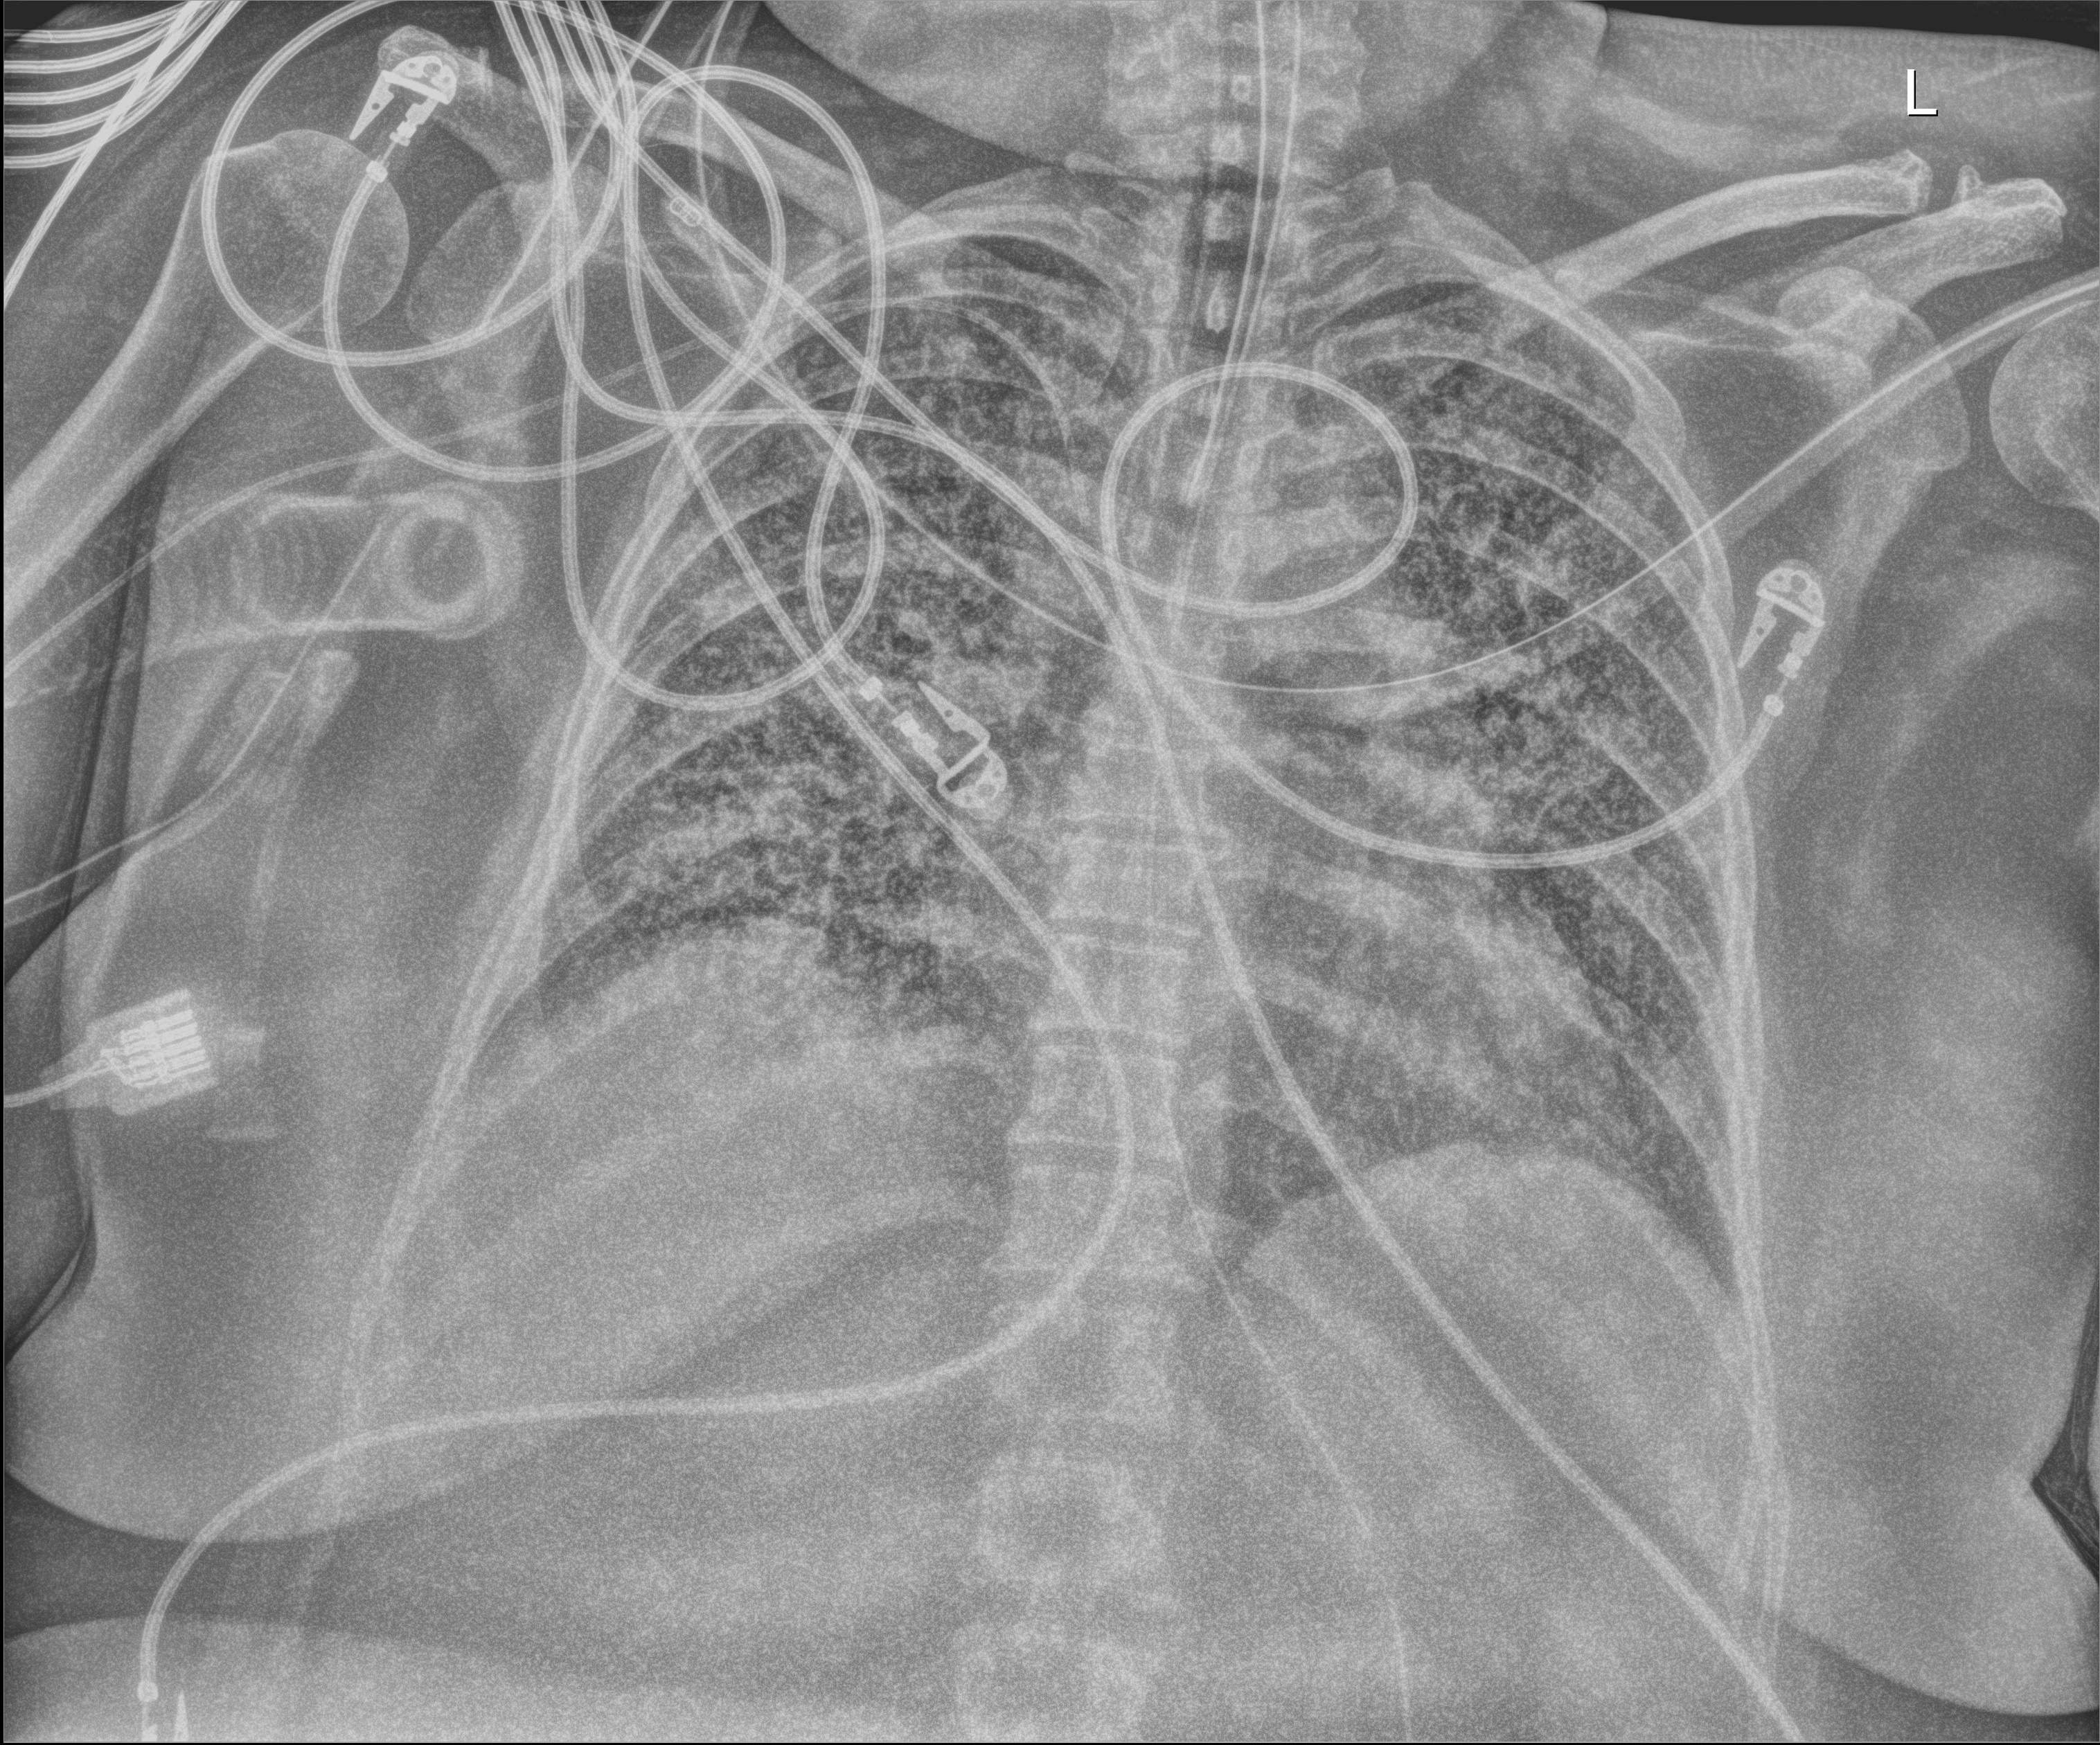
Bedside chest radiograph (digital radiography); anteroposterior (AP) projection. Patient hospitalised with COVID-19; female, aged 18–59 years.
Hospital-stay facts (about this admission, not read from this image; timing relative to this image not recorded): admitted to intensive care during this hospital stay: yes; mechanically ventilated during this hospital stay: yes.